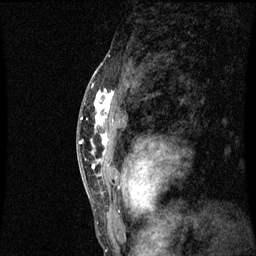
Breast MRI (dynamic contrast-enhanced), one sagittal slice. Slice 42 of 60 in the series (ordered by position). Dynamic contrast-enhanced series, image 2 of 3 at this slice position (ordered by acquisition). 1.5 T. TE 4.2 ms, TR 8.9 ms. 2 mm slice thickness. 256 × 256 image matrix, field of view 200 × 200 mm. Female patient, age 50 years. Case-level facts recorded for this patient, not image findings: setting: breast cancer imaged before/during neoadjuvant chemotherapy; receptor status: triple-negative.
Outlined on this slice (semi-automatic segmentation, software-assisted and operator-edited):
- analysis volume of interest (the breast-tissue region the enhancement analysis was run in; not a lesion): bounding box [x1, y1, x2, y2] px = [84, 80, 121, 171]
- tumour enhancement mask (voxels above the 70 % enhancement threshold inside the analysis volume of interest): [92, 90, 115, 169]